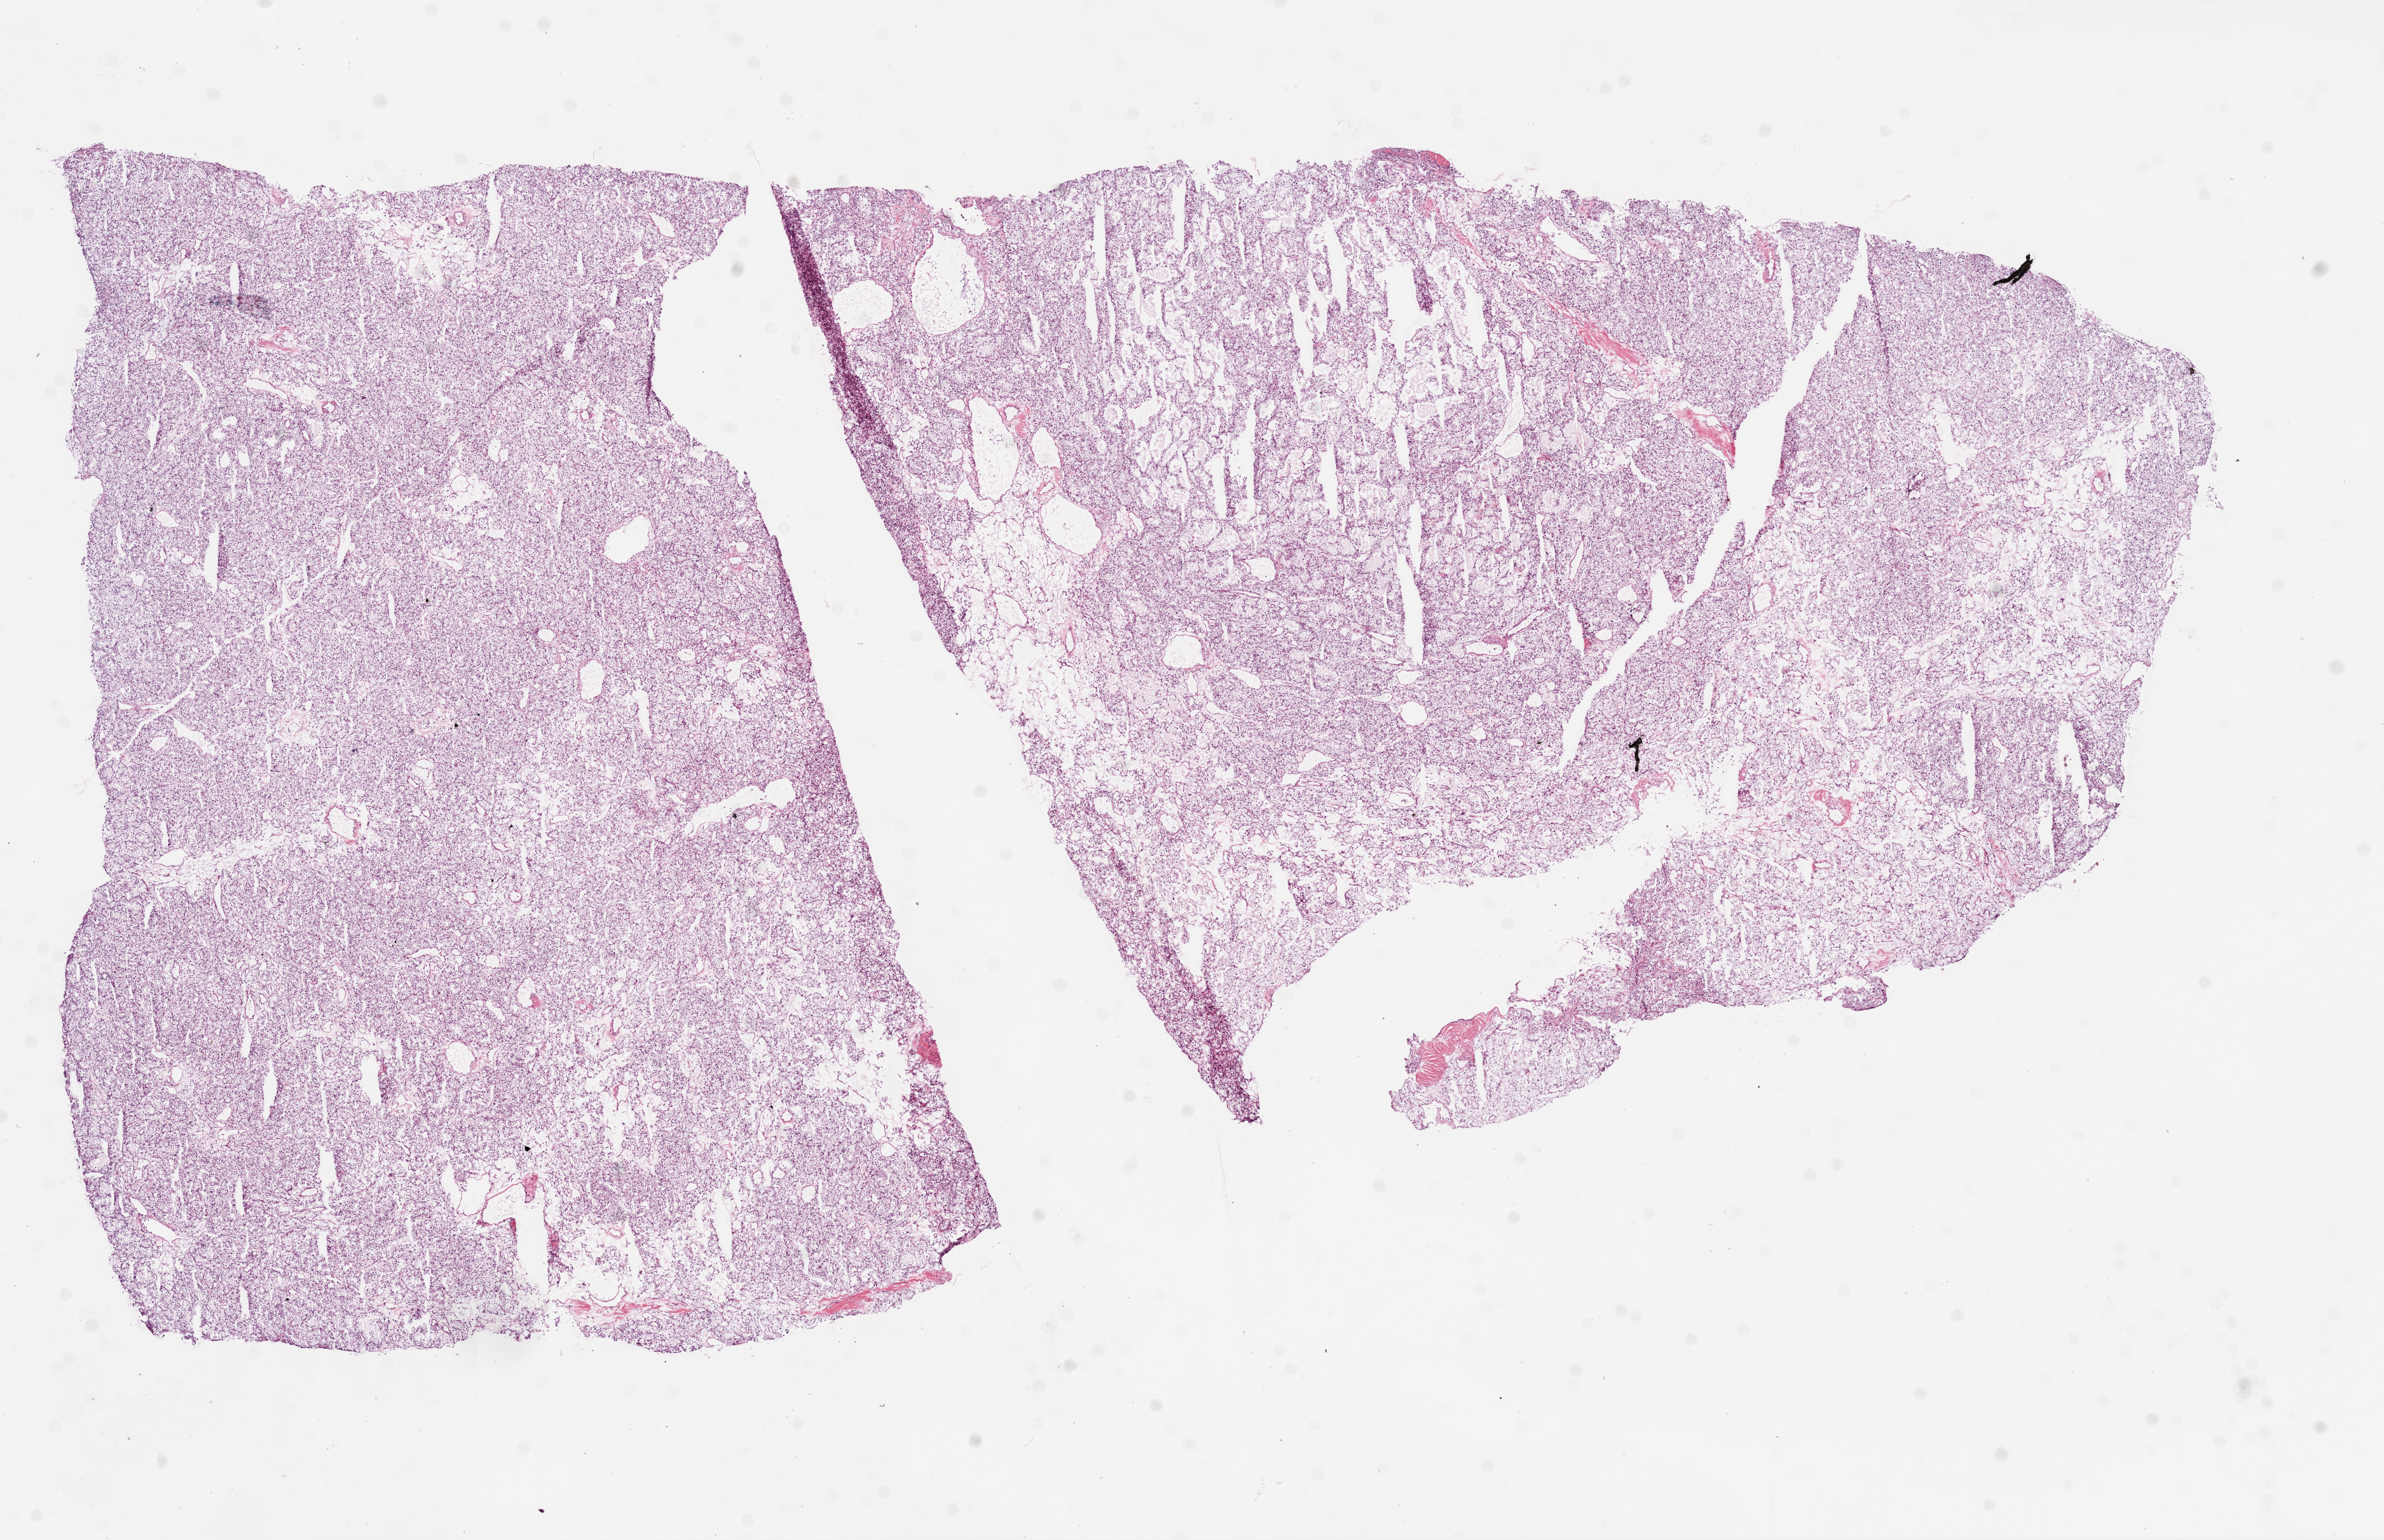
Whole-slide histology image, H&E-stained — shown as a low-resolution overview of the whole scanned area (about 15.0 x 9.7 mm); frozen section from the bottom of the tissue portion; kidney, primary tumour sample. Patient: male, age at initial diagnosis 54 years. Histologic grade: G2 (moderately differentiated). Composition of this section per pathologist review: tumour cells 90%, tumour nuclei 85%, normal cells 0%, stromal cells 10%, necrosis 0%.
• histologic diagnosis: Clear cell adenocarcinoma, NOS
• laterality: right
• AJCC pathologic stage: I
• TNM: T1a NX M0